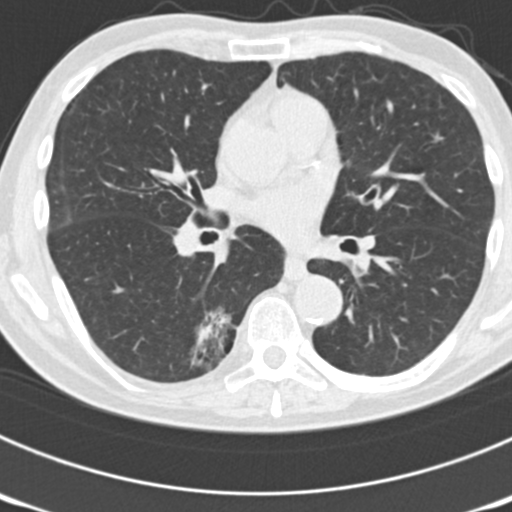
Low-dose screening chest CT, axial slice, third screening round (two years after baseline), lung window (W 1500 / L -600 HU), 2 mm slice thickness, 120 kVp, slice 81 of 177 in the series. Male, age 70 years at enrolment. Current smoker at enrolment.
Lesion marked by an expert reader, bounding box <147,303,238,385> (left, top, right, bottom; pixels). The screening reader recorded 3 non-calcified nodules or masses ≥4 mm on this exam; which of them this box marks is not recorded. Official screen result: positive, other.